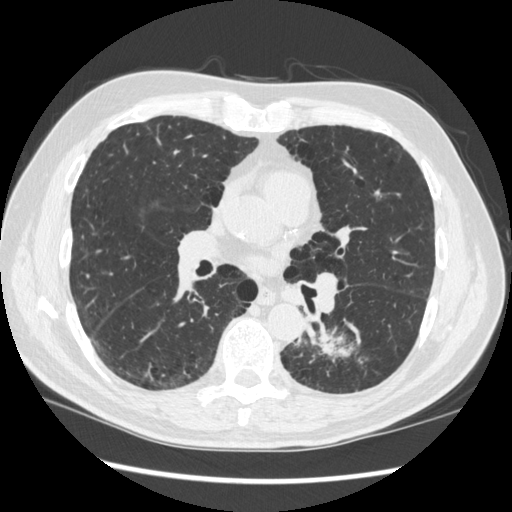
Low-dose screening chest CT, one axial slice. Position 168 of 348 along the scan axis. Reconstruction kernel STANDARD. 120 kVp. Lung window (W 1500 / L -600 HU). 1.25 mm slice thickness. 512 × 512 image matrix.
Structures marked on this image (outlined manually by an expert reader):
- lesion 1 (tumor, lower lobe of left lung): bounding box (x1, y1, x2, y2) in pixels: (312, 332, 362, 363)